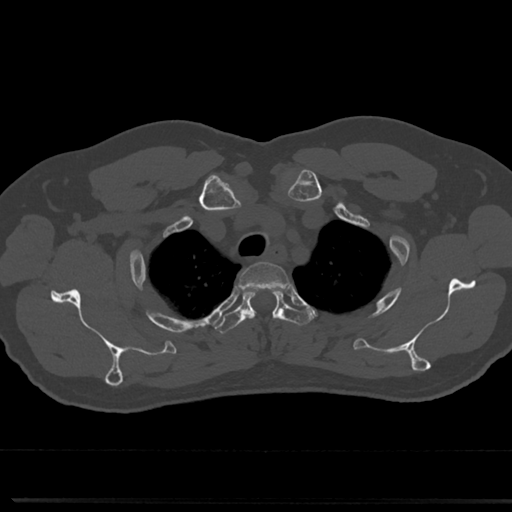
CT including the spine, one axial slice. Slice 607 of 817 in the series (ordered by position). 120 kVp. Bone window (W 1800 / L 400 HU). 0.5 mm slice thickness. 512 × 512 image matrix, field of view 355 × 355 mm. Patient: male, 61 years. From the clinical record (not read from this slice): primary cancer: prostate.
Outlined on this slice (semi-automatic segmentation, software-assisted and operator-edited):
- T2 vertebra: bounding box [x1, y1, x2, y2] px = [239, 262, 288, 285]
- T3 vertebra: [215, 286, 305, 333]